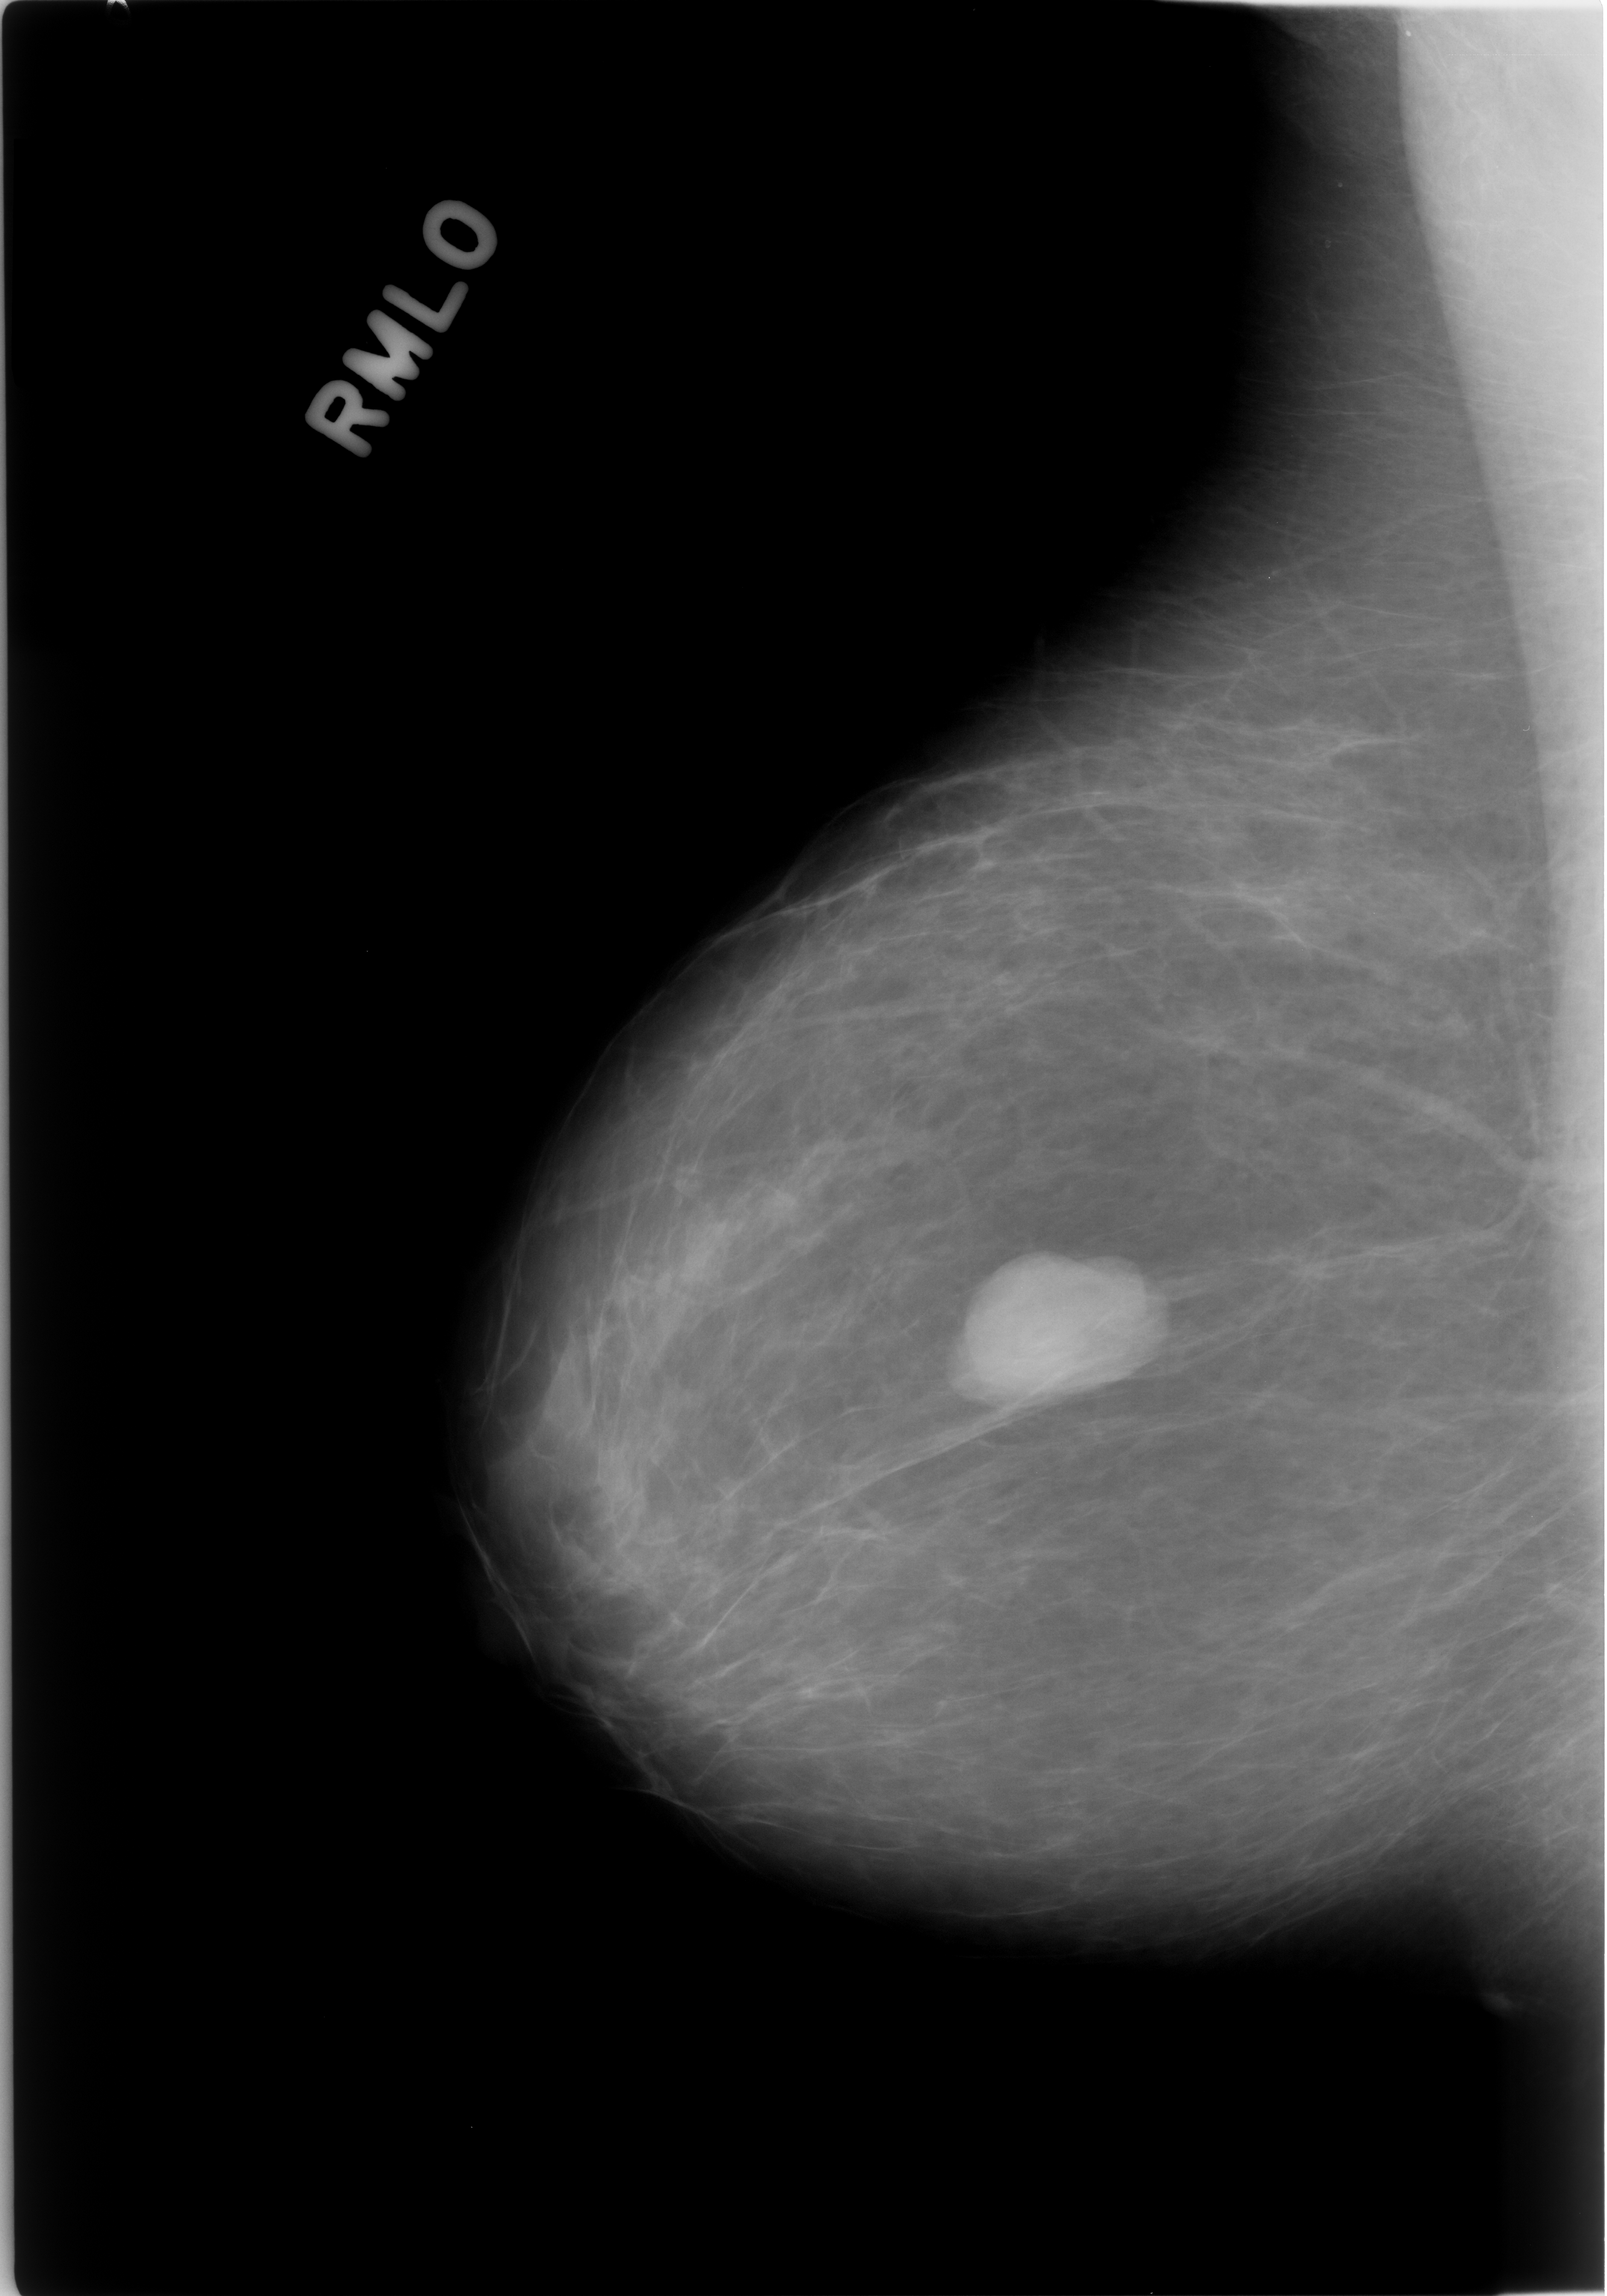
Digitized screen-film mammogram. Right breast. Mediolateral oblique (MLO) view. BI-RADS breast density category 1 (scale 1–4). 1607 × 2296 image matrix.
Expert-marked regions of interest on this film, with their recorded descriptors:
- mass, shape lobulated, margins circumscribed; BI-RADS assessment category 4; pathology (as recorded): benign: box from (x=948, y=1243) to (x=1152, y=1420) px